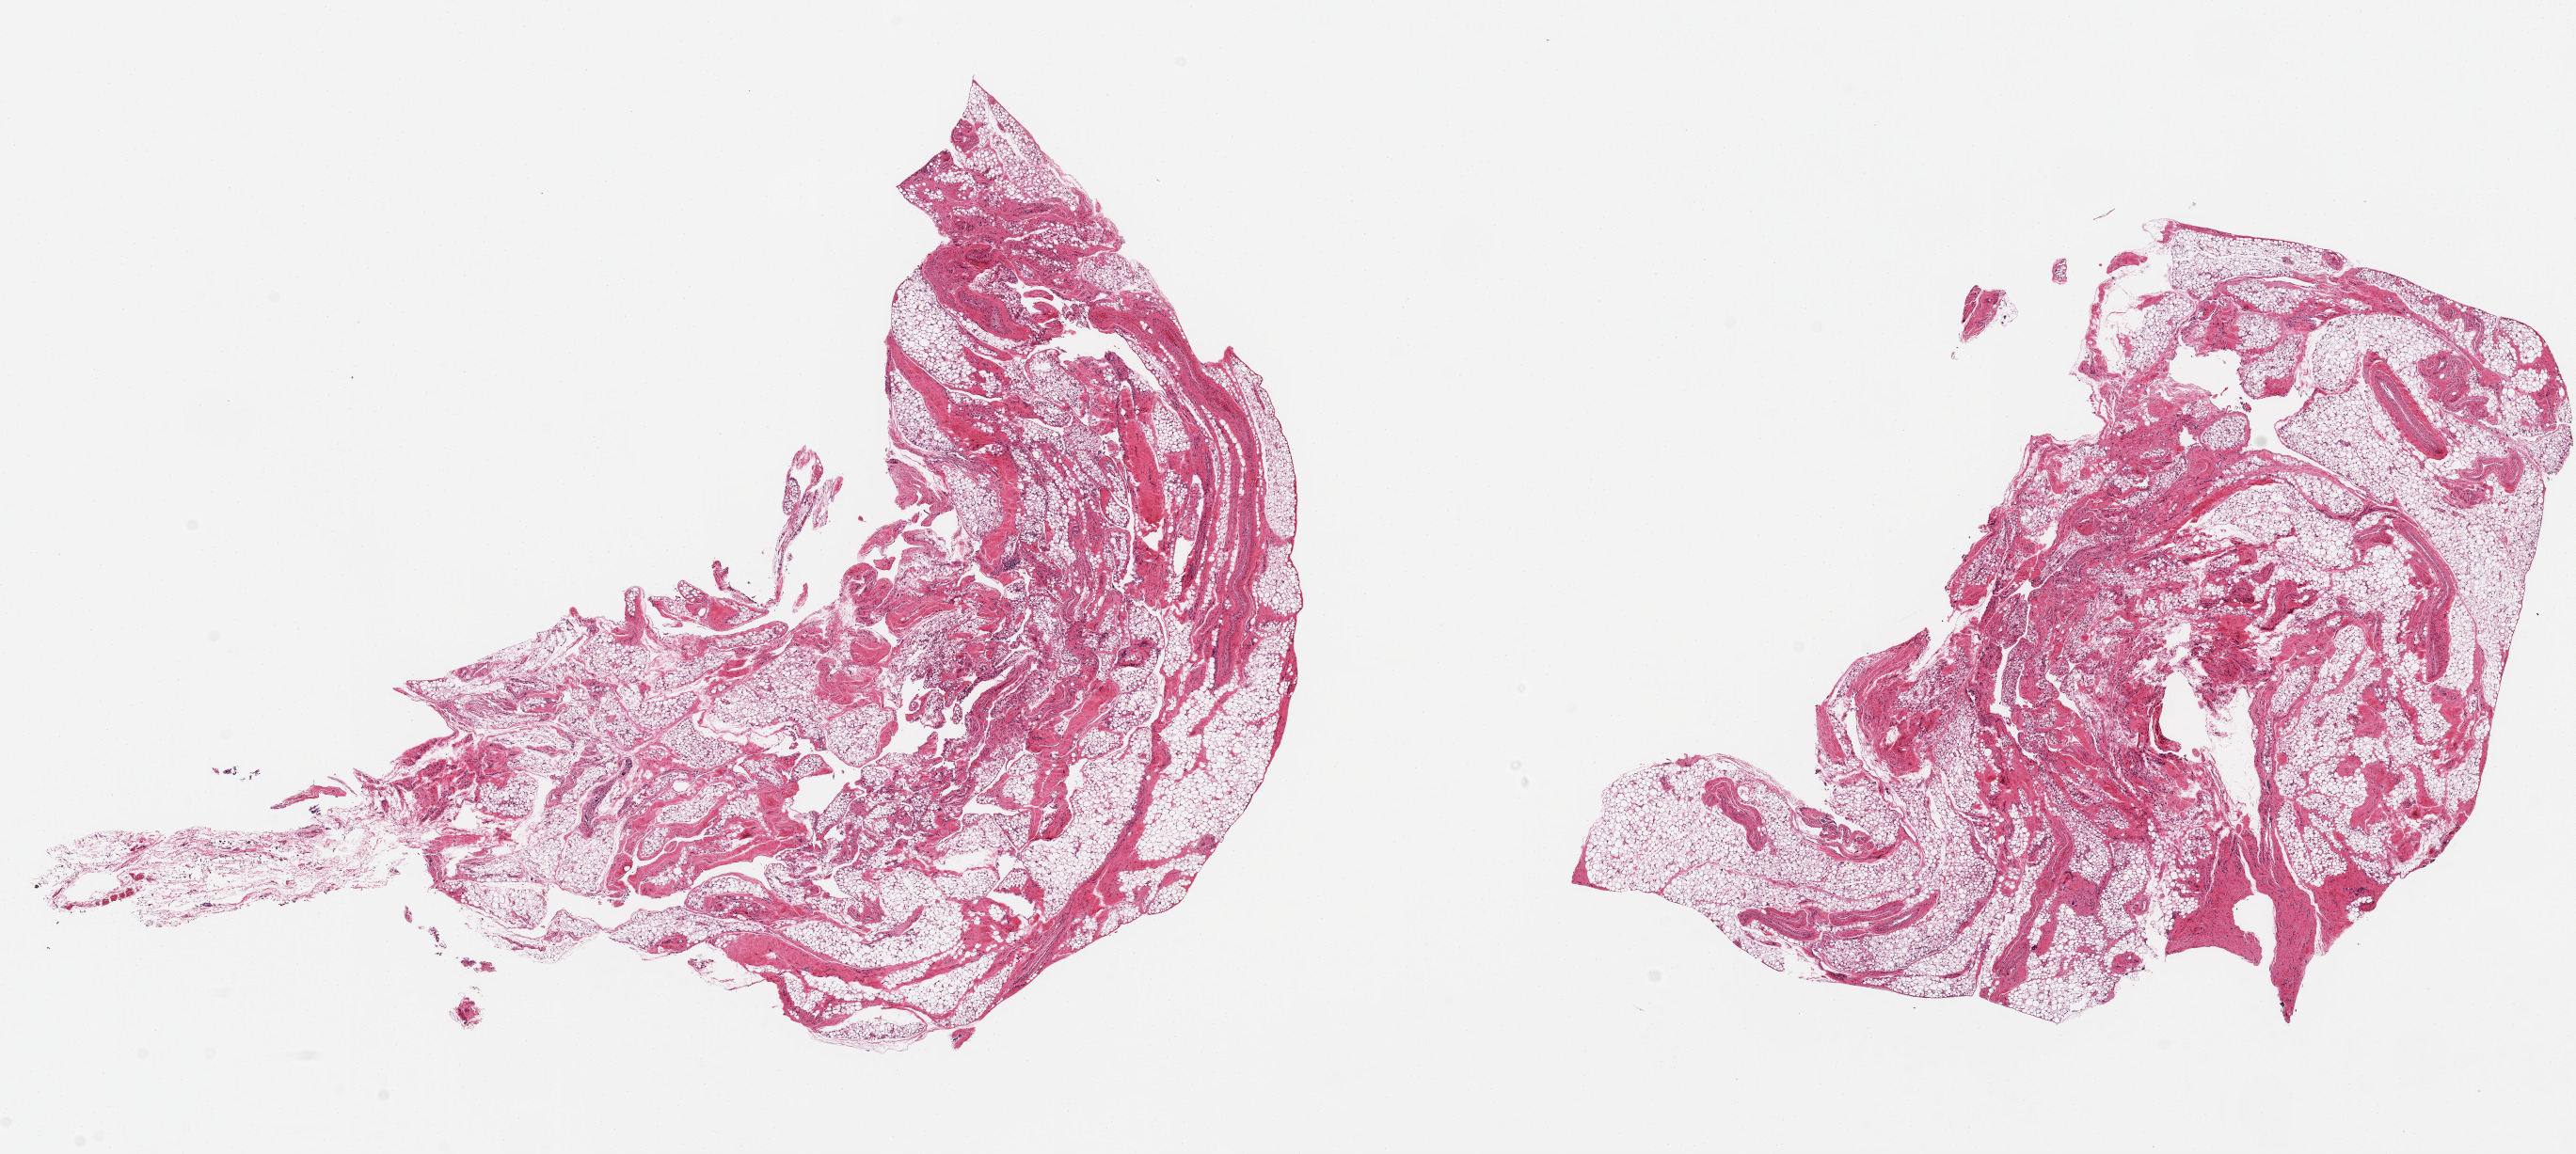
Haematoxylin and eosin whole-slide image — whole scanned area (about 21.7 x 9.7 mm, acquisition: 20x scan) shown as a low-resolution overview, PAXgene-fixed paraffin-embedded (PFPE) section, target tissue: omentum, donor tissue sample. Male donor.
• pathologist's review note for this sample: 2 pieces, ~40% fascia/mesothelial hyperplasia and vascular elements